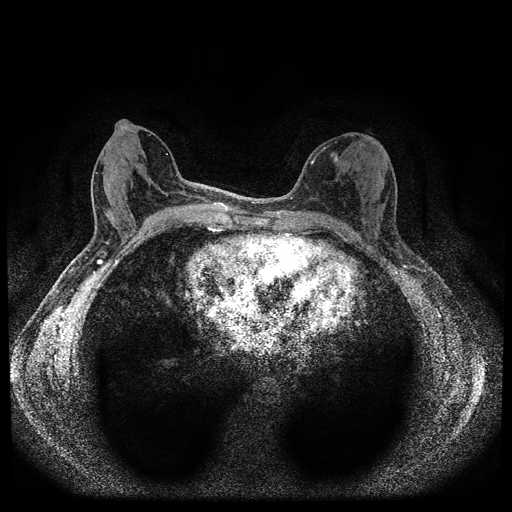
Breast MRI (dynamic contrast-enhanced, multi-phase), one axial slice. Slice 44 of 112 in the series (ordered by position). Dynamic contrast-enhanced series, time point 2 of 5 at this slice position (early post-contrast). 1.5 T. TE 2.7 ms, TR 5.4 ms. 2 mm slice thickness. 512 × 512 image matrix, field of view 320 × 320 mm. Patient: female, 61 years.
Outlined on this slice (semi-automatically segmented with operator editing):
- breast lesion (labelled benign in the annotation): bounding box [x1, y1, x2, y2] px = [331, 152, 338, 163]